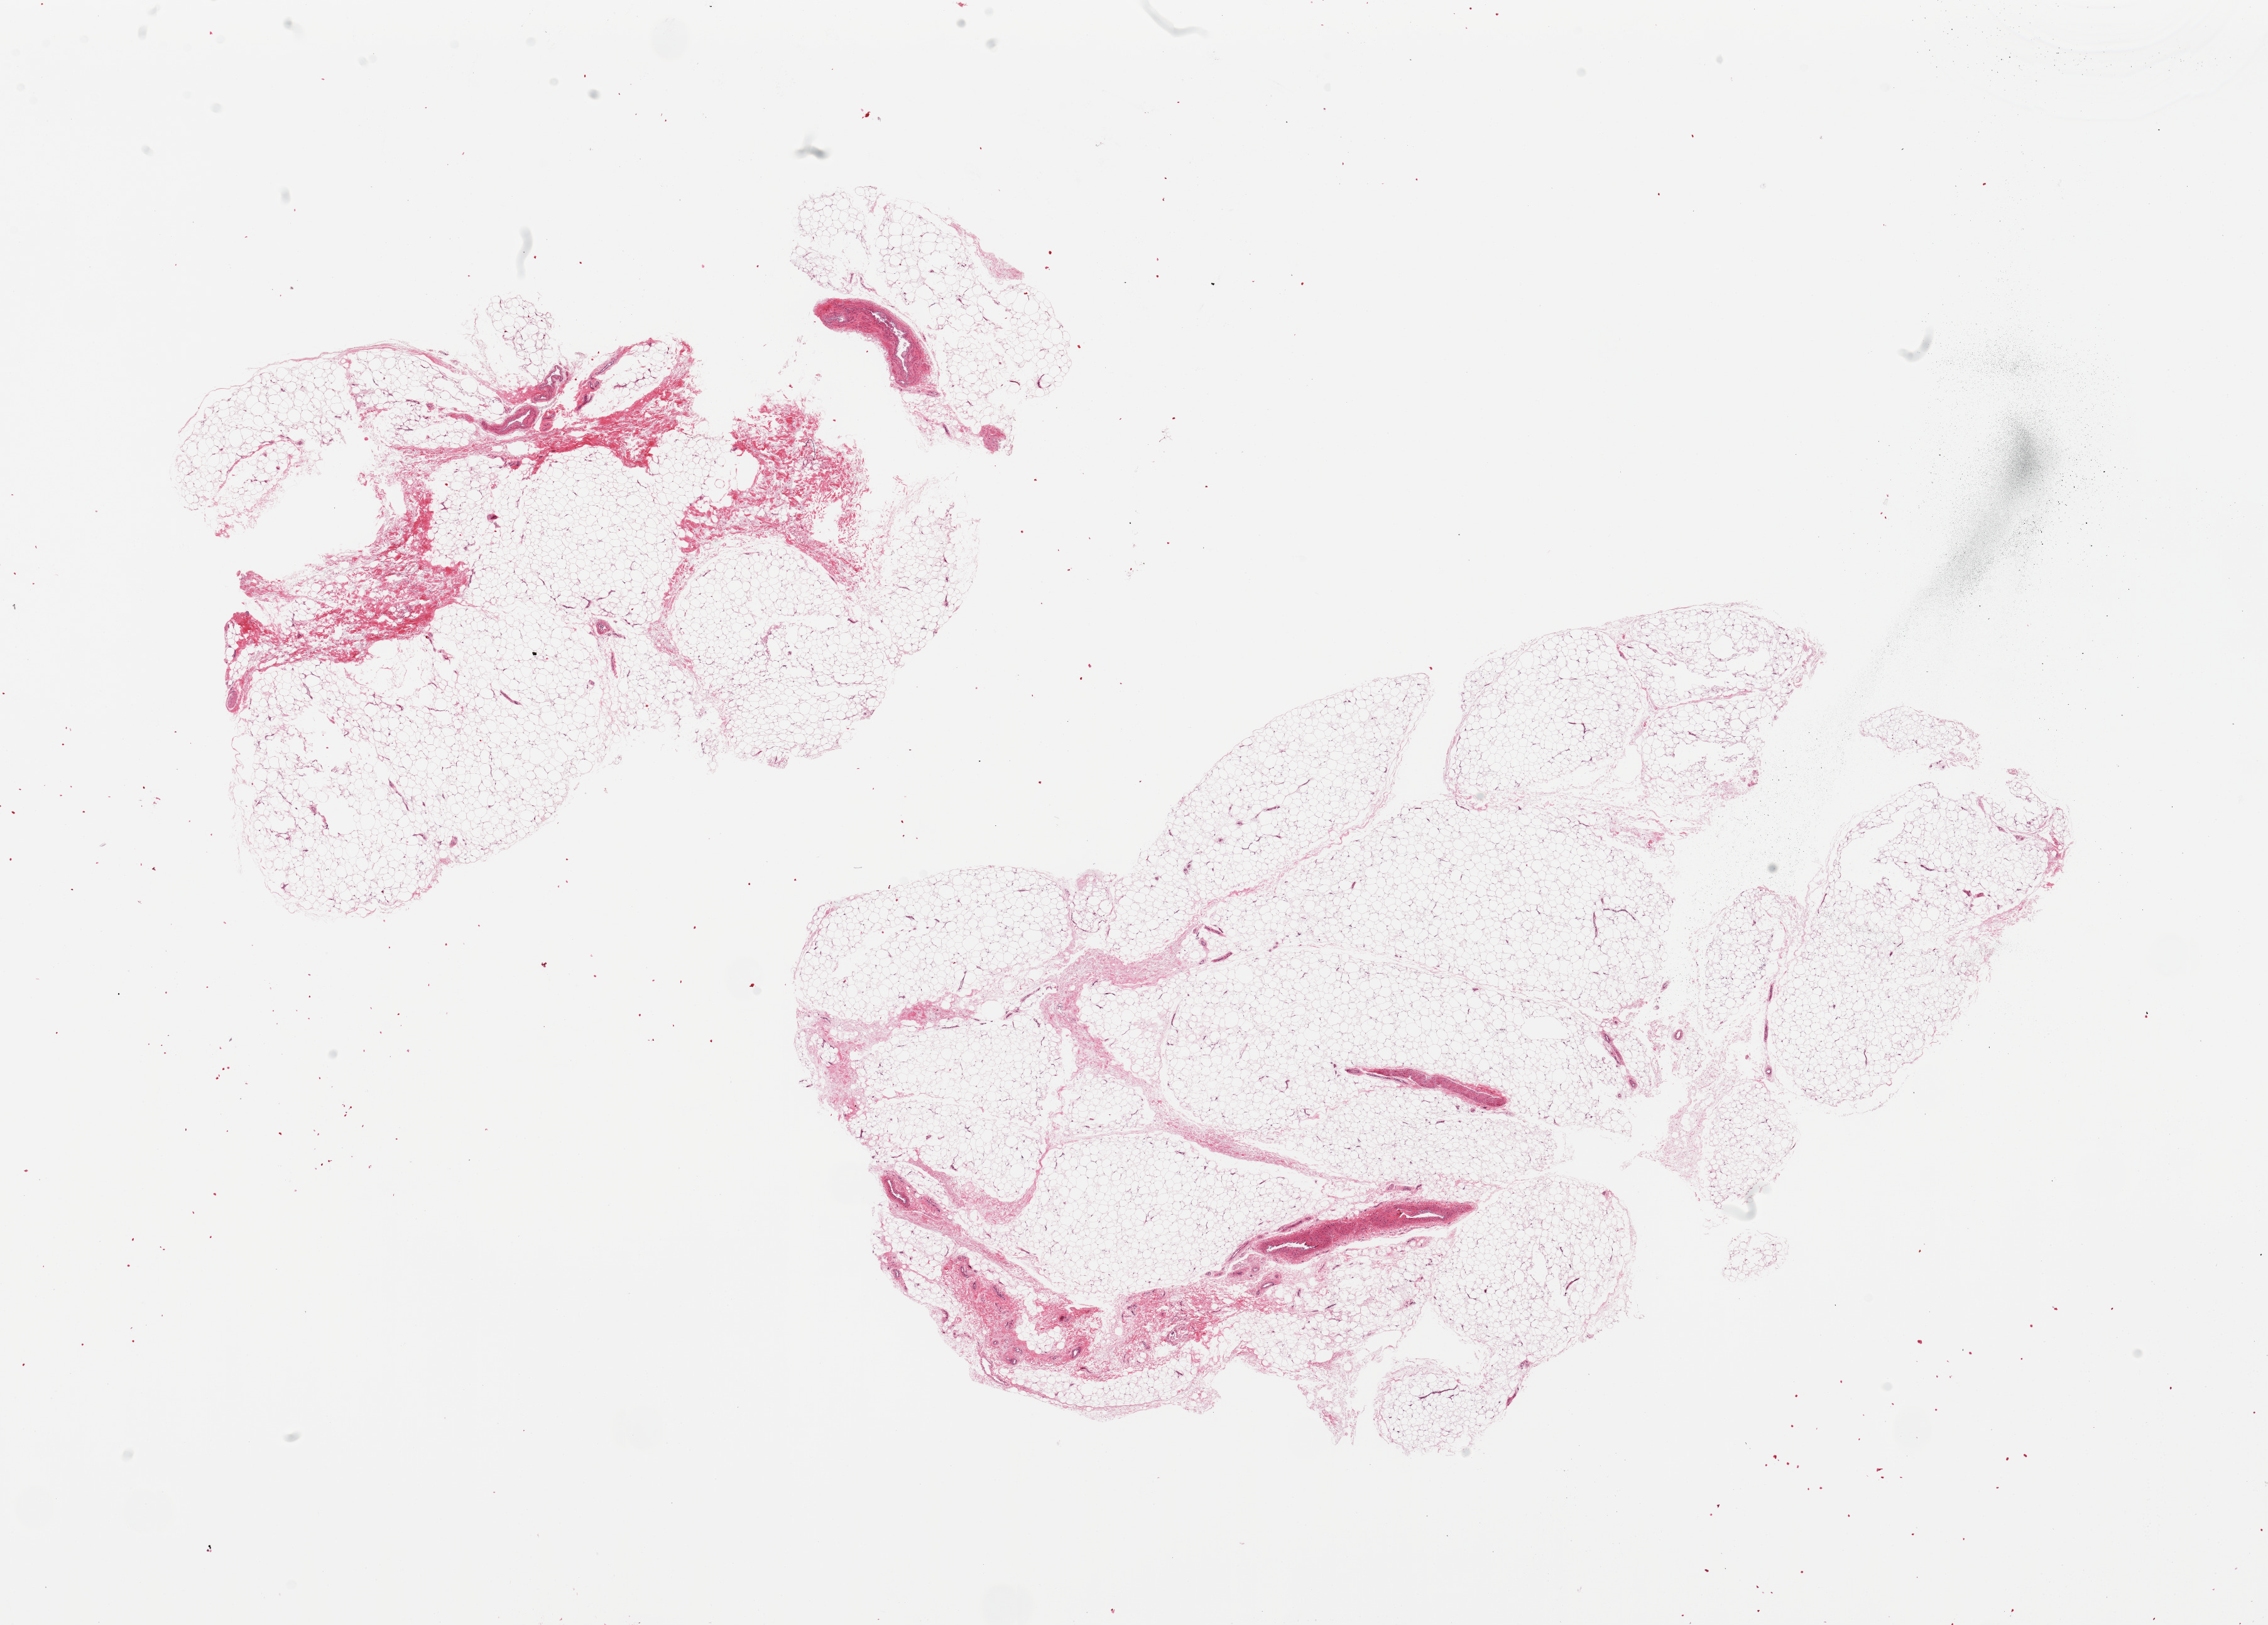
Whole-slide image, haematoxylin and eosin stain, brightfield, whole scanned area (about 28.5 x 20.5 mm, acquisition: 20x scan) shown as a low-resolution overview. PAXgene-fixed, paraffin-embedded tissue. Section of adipose tissue (target tissue). Donor tissue sample. Donor sex: male.
• pathologist's review note for this sample: 2 pieces